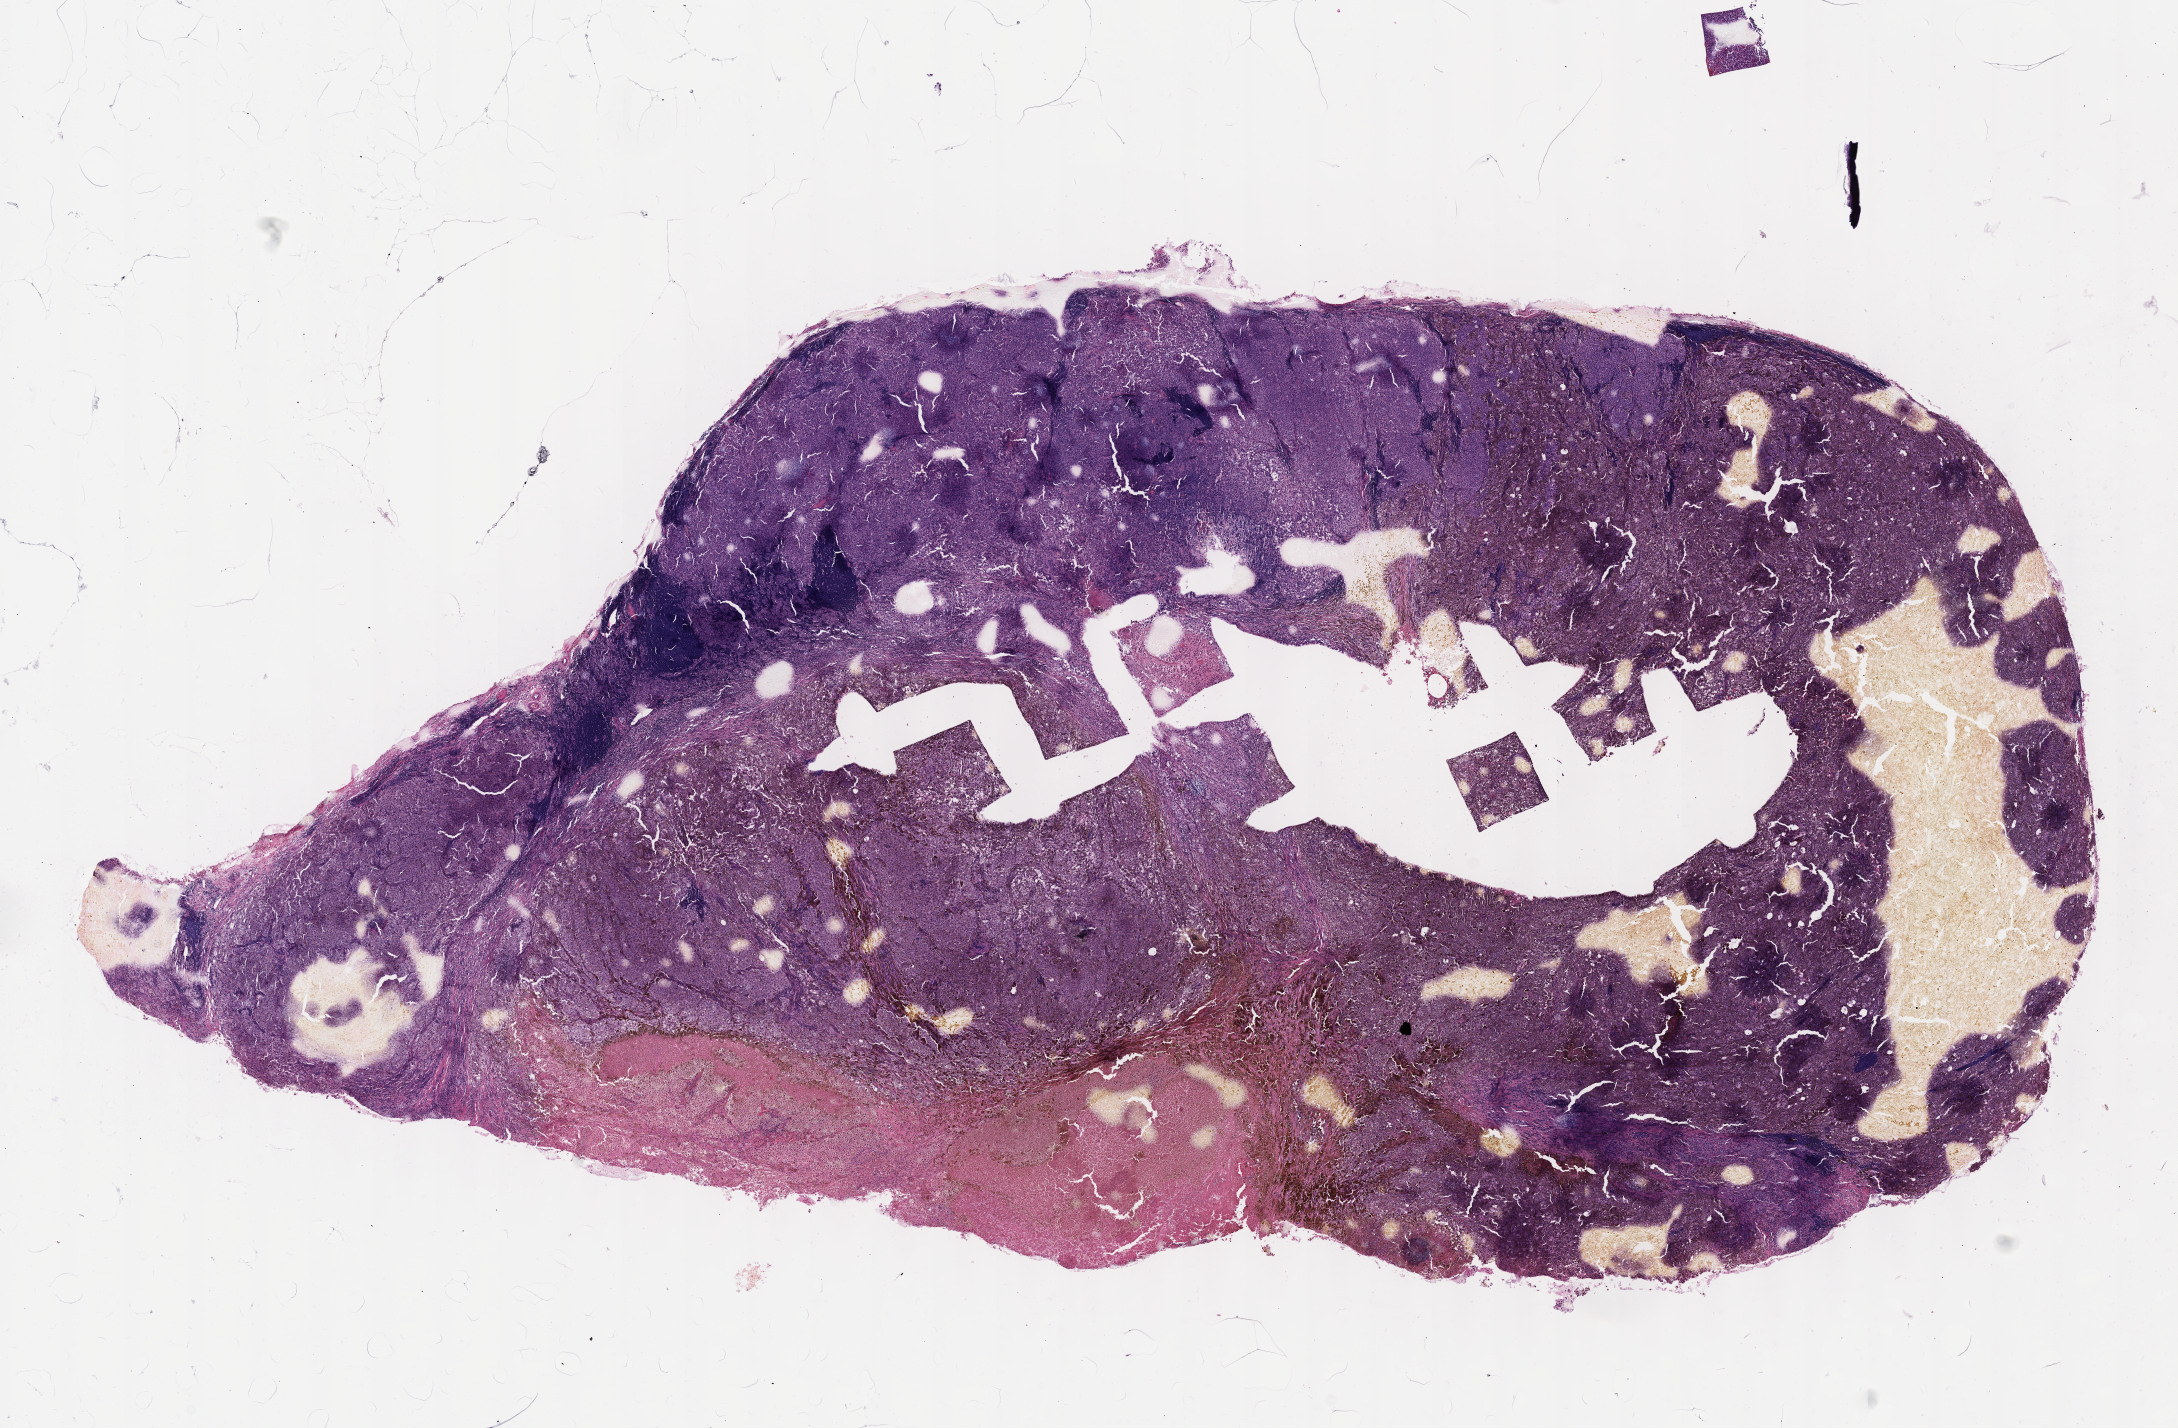
Digitized Hematoxylin and eosin (H&E) stained tissue section (whole slide), shown as a low-resolution overview of the whole scanned area (about 17.6 x 11.5 mm). Formalin-fixed paraffin-embedded (FFPE) diagnostic section. Sample: primary tumour, skin. Patient: female, age at initial diagnosis 40 years.
- AJCC pathologic stage: IV (7th edition)
- diagnosis: Malignant melanoma, NOS